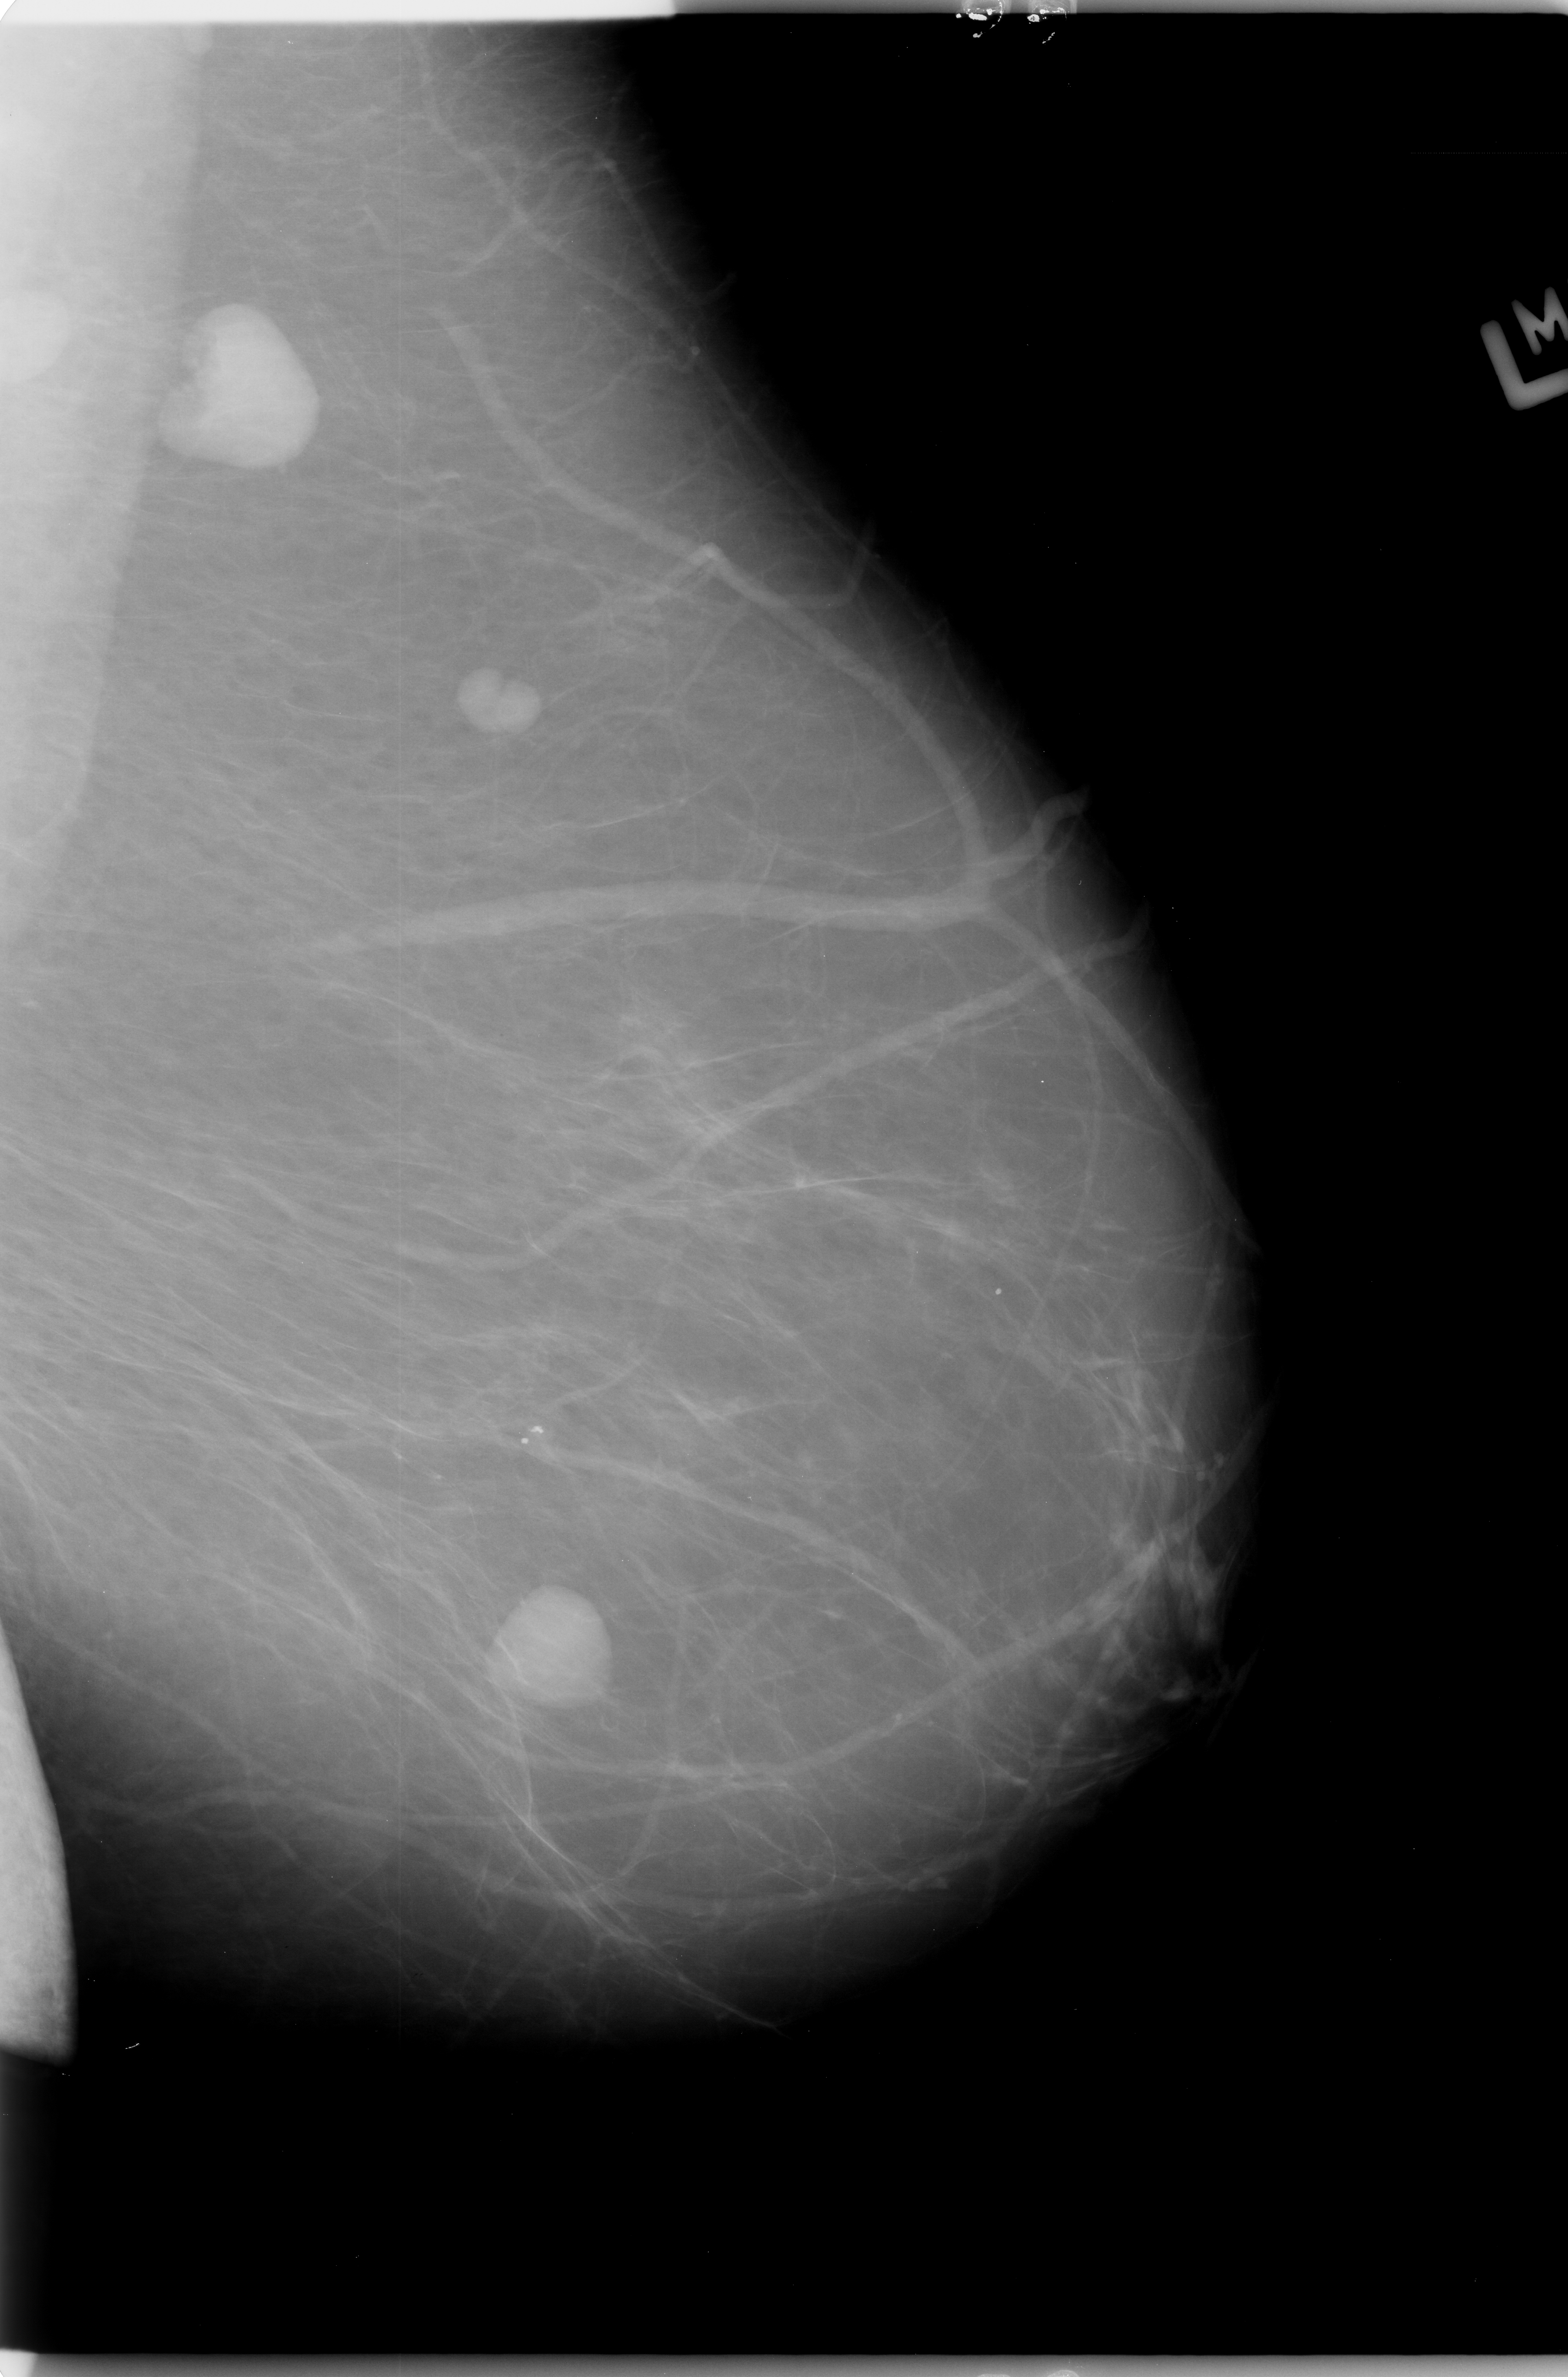
Mammogram (digitized film). Left breast. MLO view. BI-RADS breast density category 1 (scale 1–4). 1568 × 2377 image matrix.
Marked abnormalities (boxes around the expert regions of interest):
- mass, shape oval, margins circumscribed; BI-RADS assessment category 4; subtlety rating 5 on a 1 (subtle) to 5 (obvious) scale; pathology result (as recorded, not read from the image): benign: bounding box <493,1584,606,1692> (left, top, right, bottom; pixels)